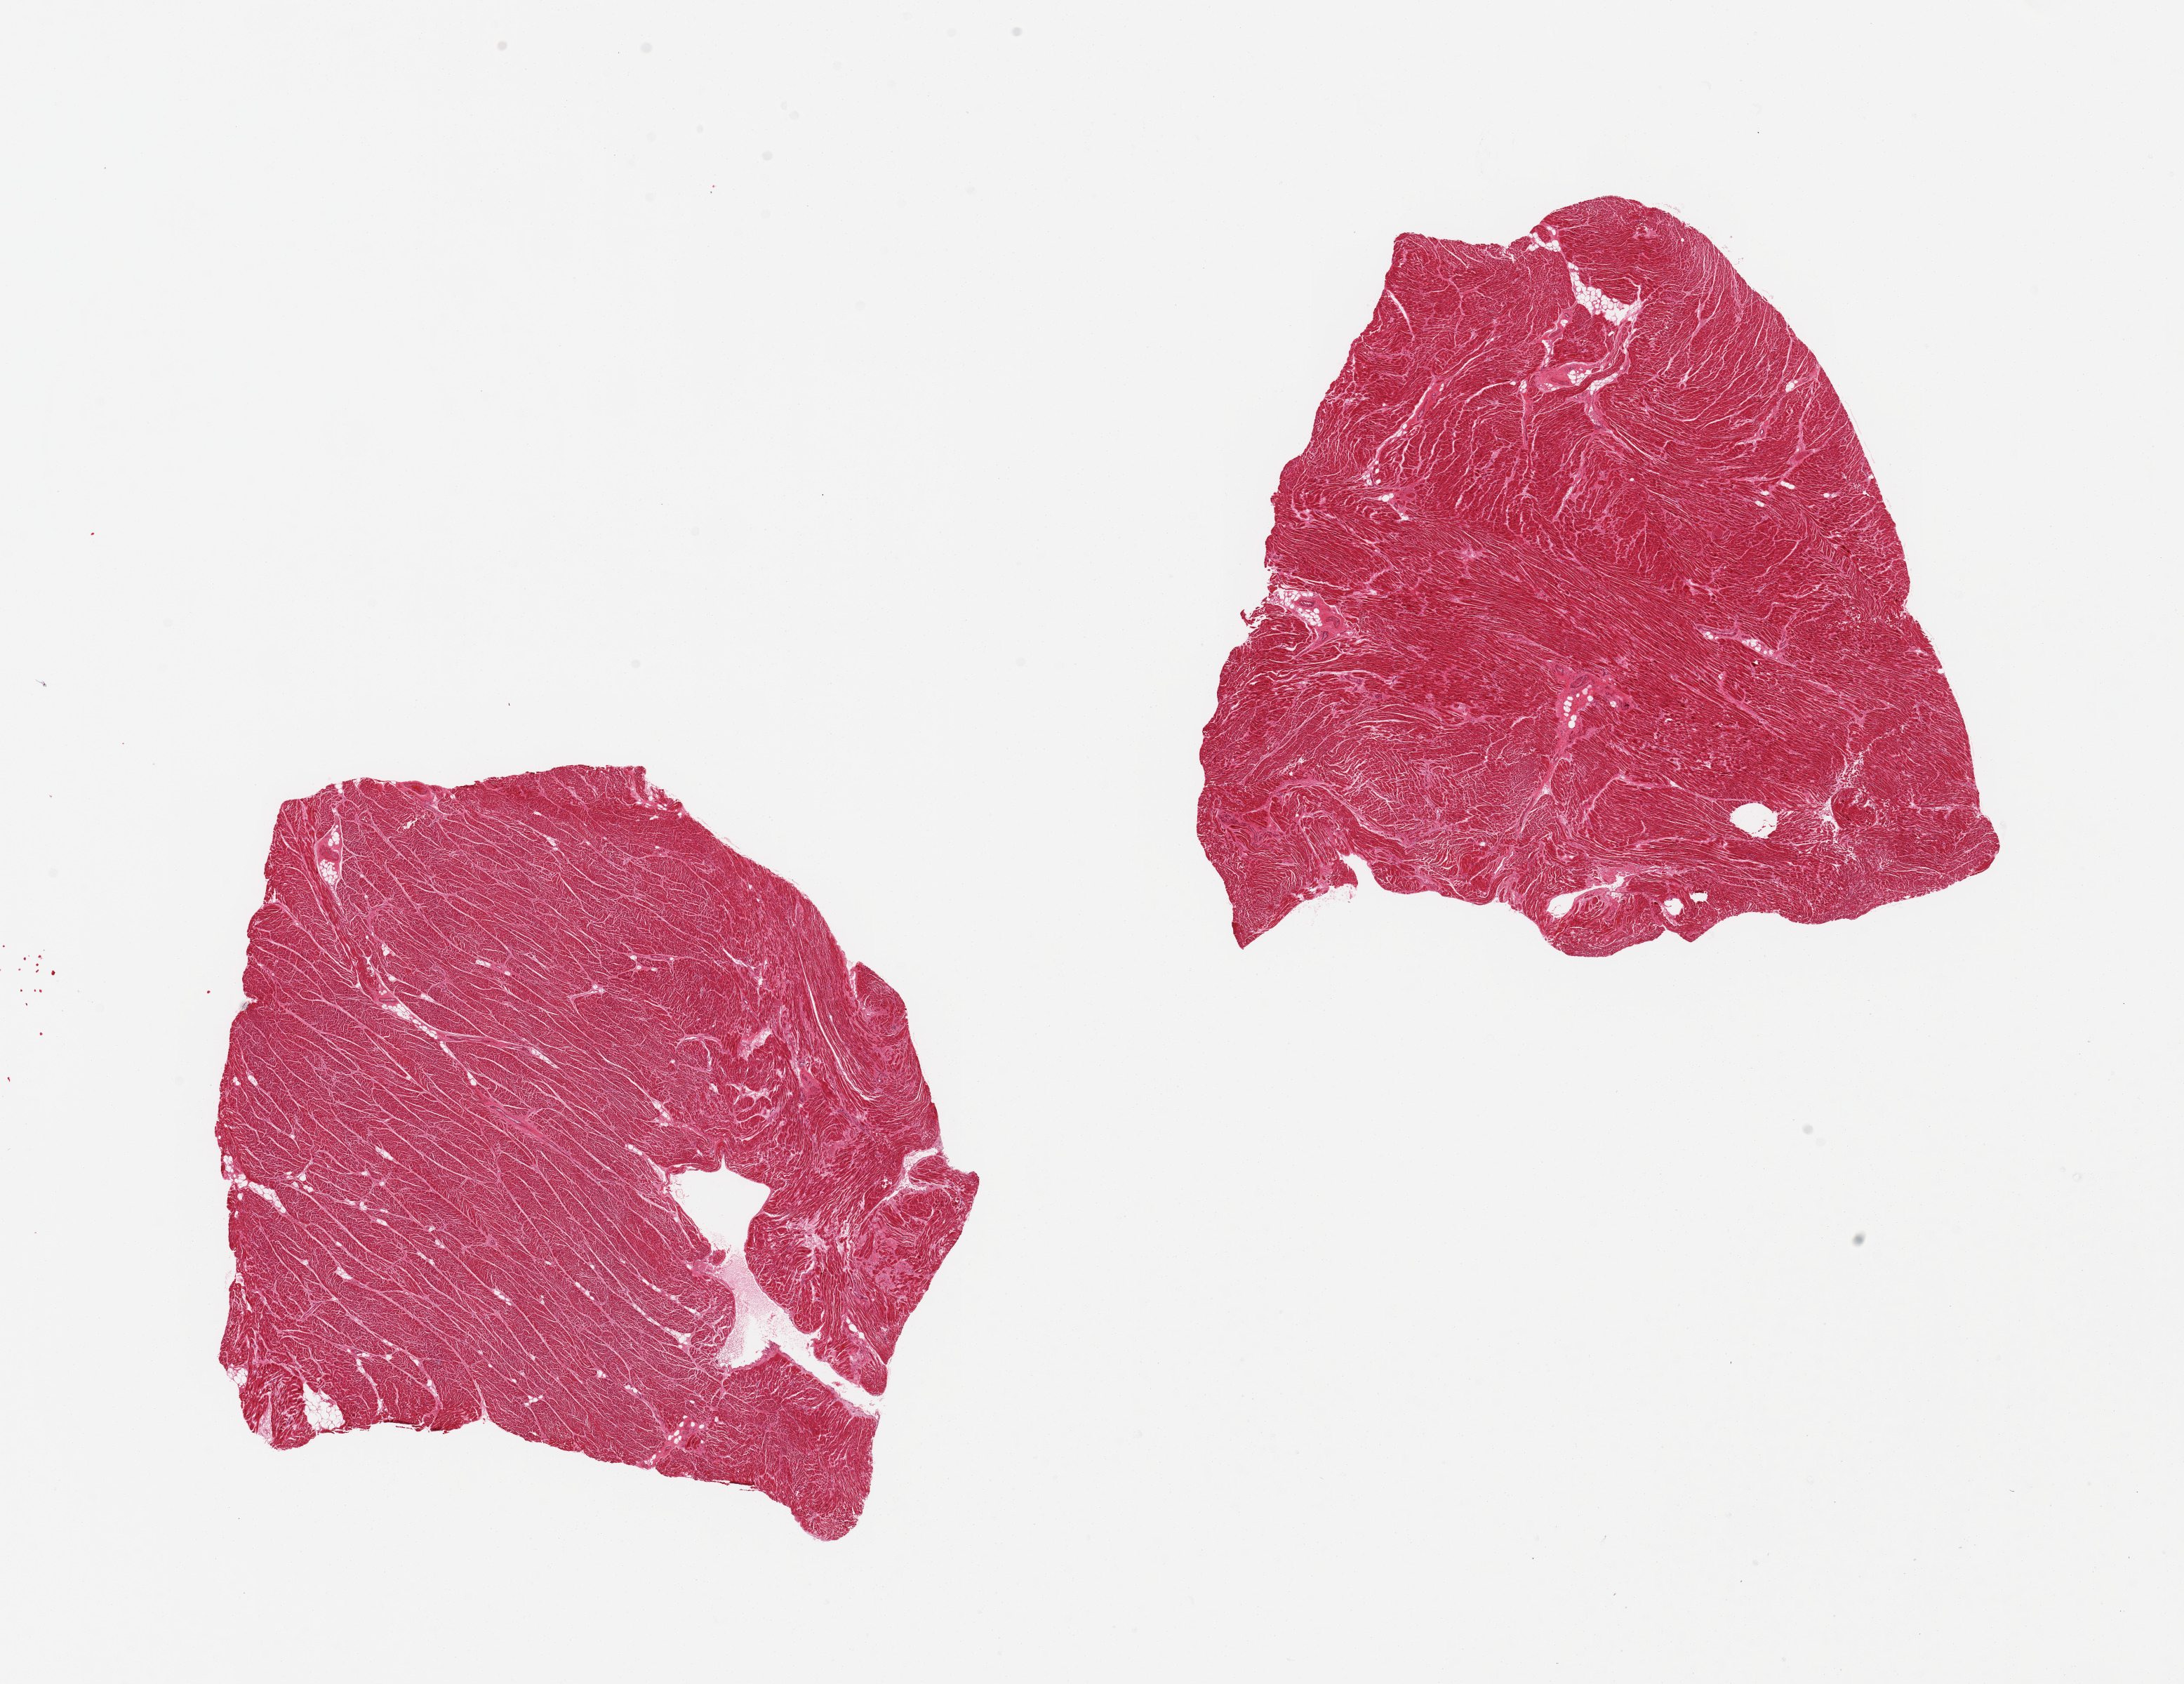
Haematoxylin and eosin whole-slide image — shown as a low-resolution overview of the whole scanned area (about 24.6 x 19.0 mm), PAXgene-fixed, paraffin-embedded tissue, section of heart (target tissue), tissue donor sample.
Reviewer comment on this tissue sample: 2 pieces, minimal interstitial fibrosis.